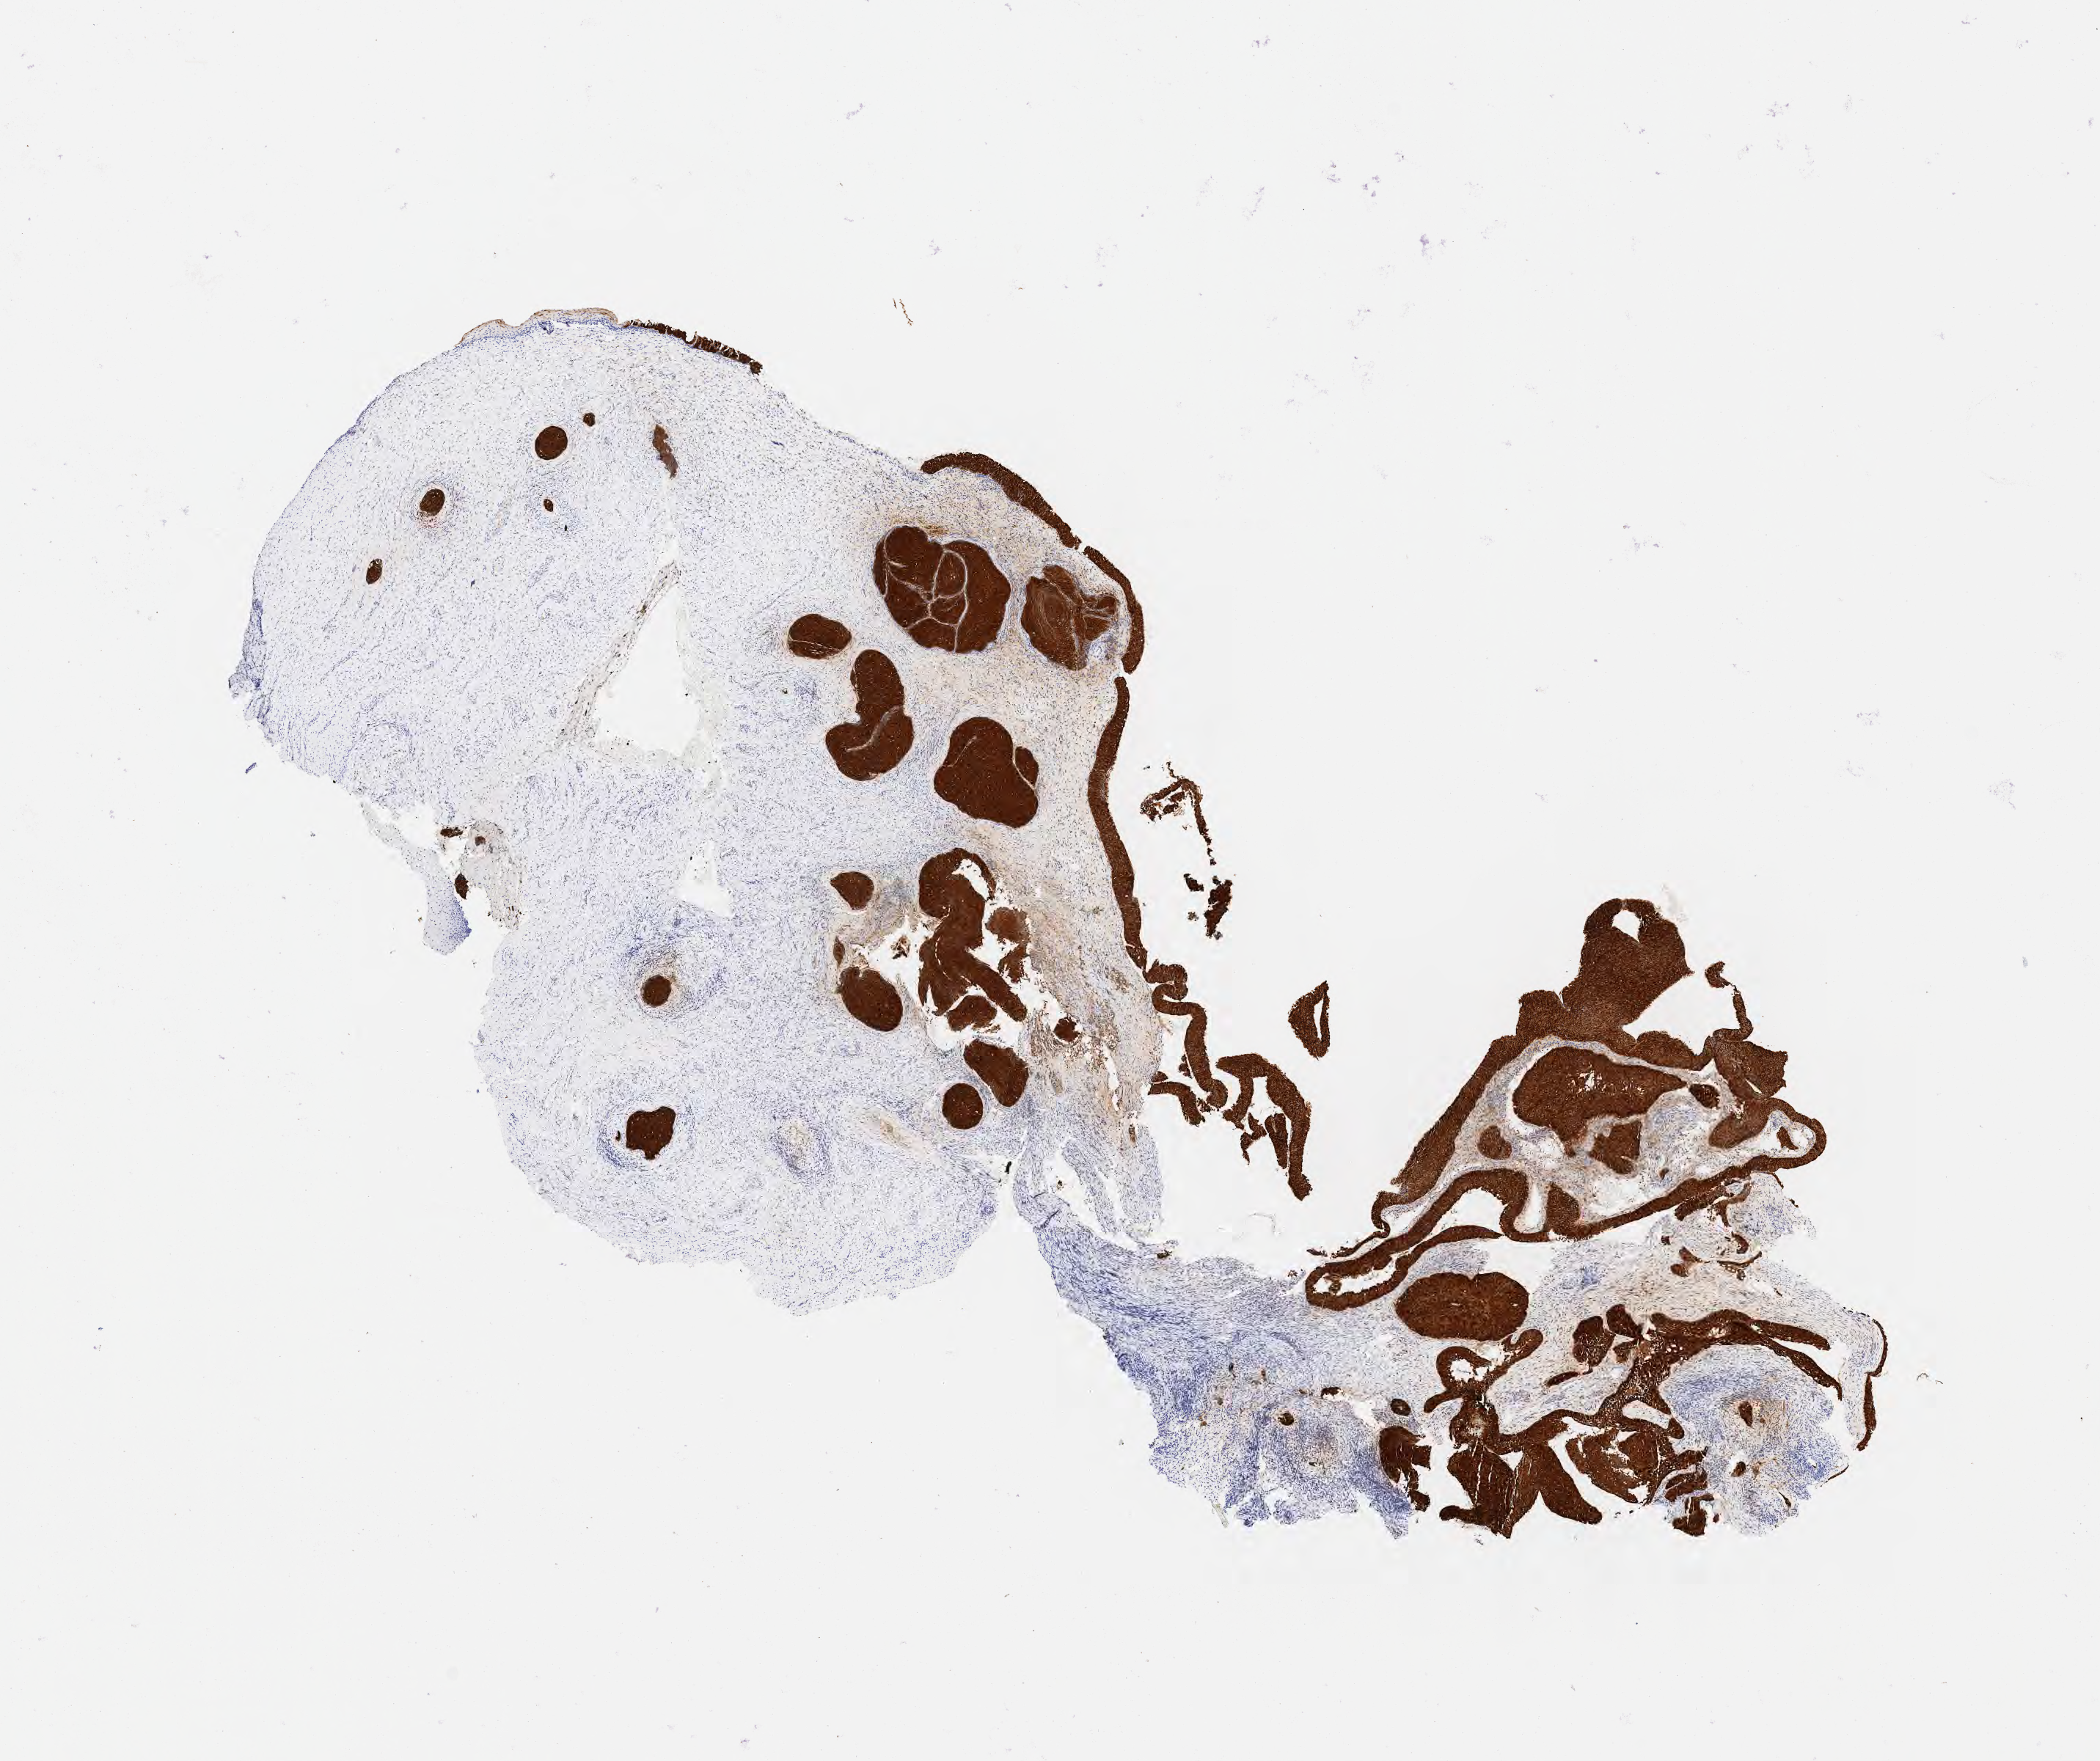
Immunohistochemistry (IHC) whole-slide image stained for p16 (p16INK4a) — a low-resolution overview of the entire scanned area, about 11.6 x 9.7 mm; specimen: tumor tissue; site: cervix. Female patient, aged 54.
- diagnosis: Squamous cell carcinoma, large cell, nonkeratinizing, NOS